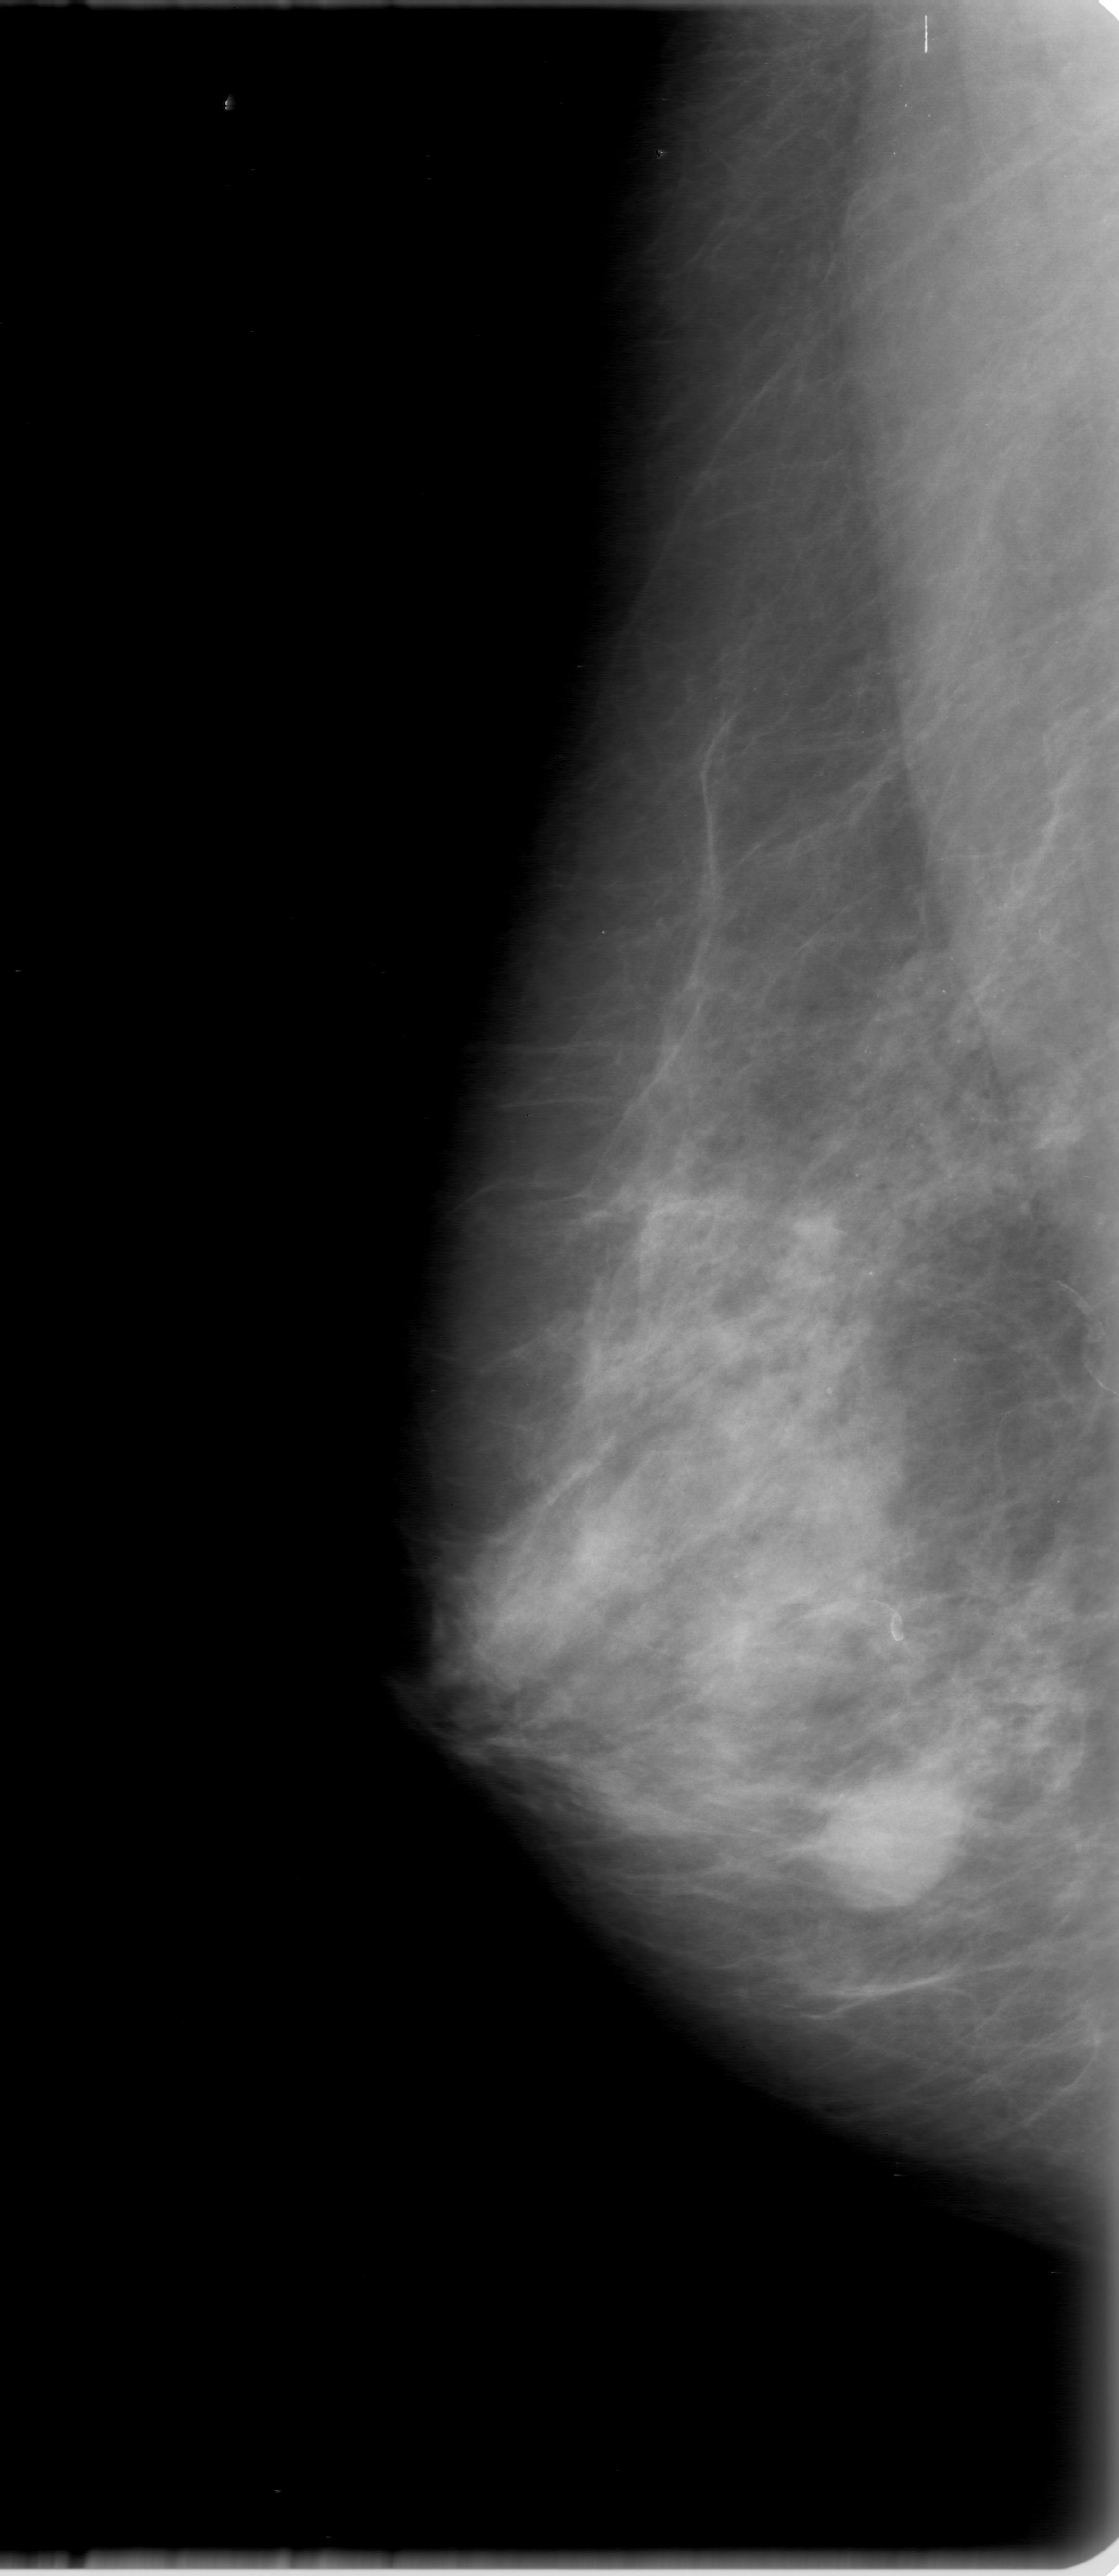
Mammogram (digitized film), right breast, mediolateral oblique (MLO) view.
Finding: mass, shape oval, margins obscured; BI-RADS assessment category 0; subtlety rating 5 on a 1 (subtle) to 5 (obvious) scale; pathology (as recorded): benign.